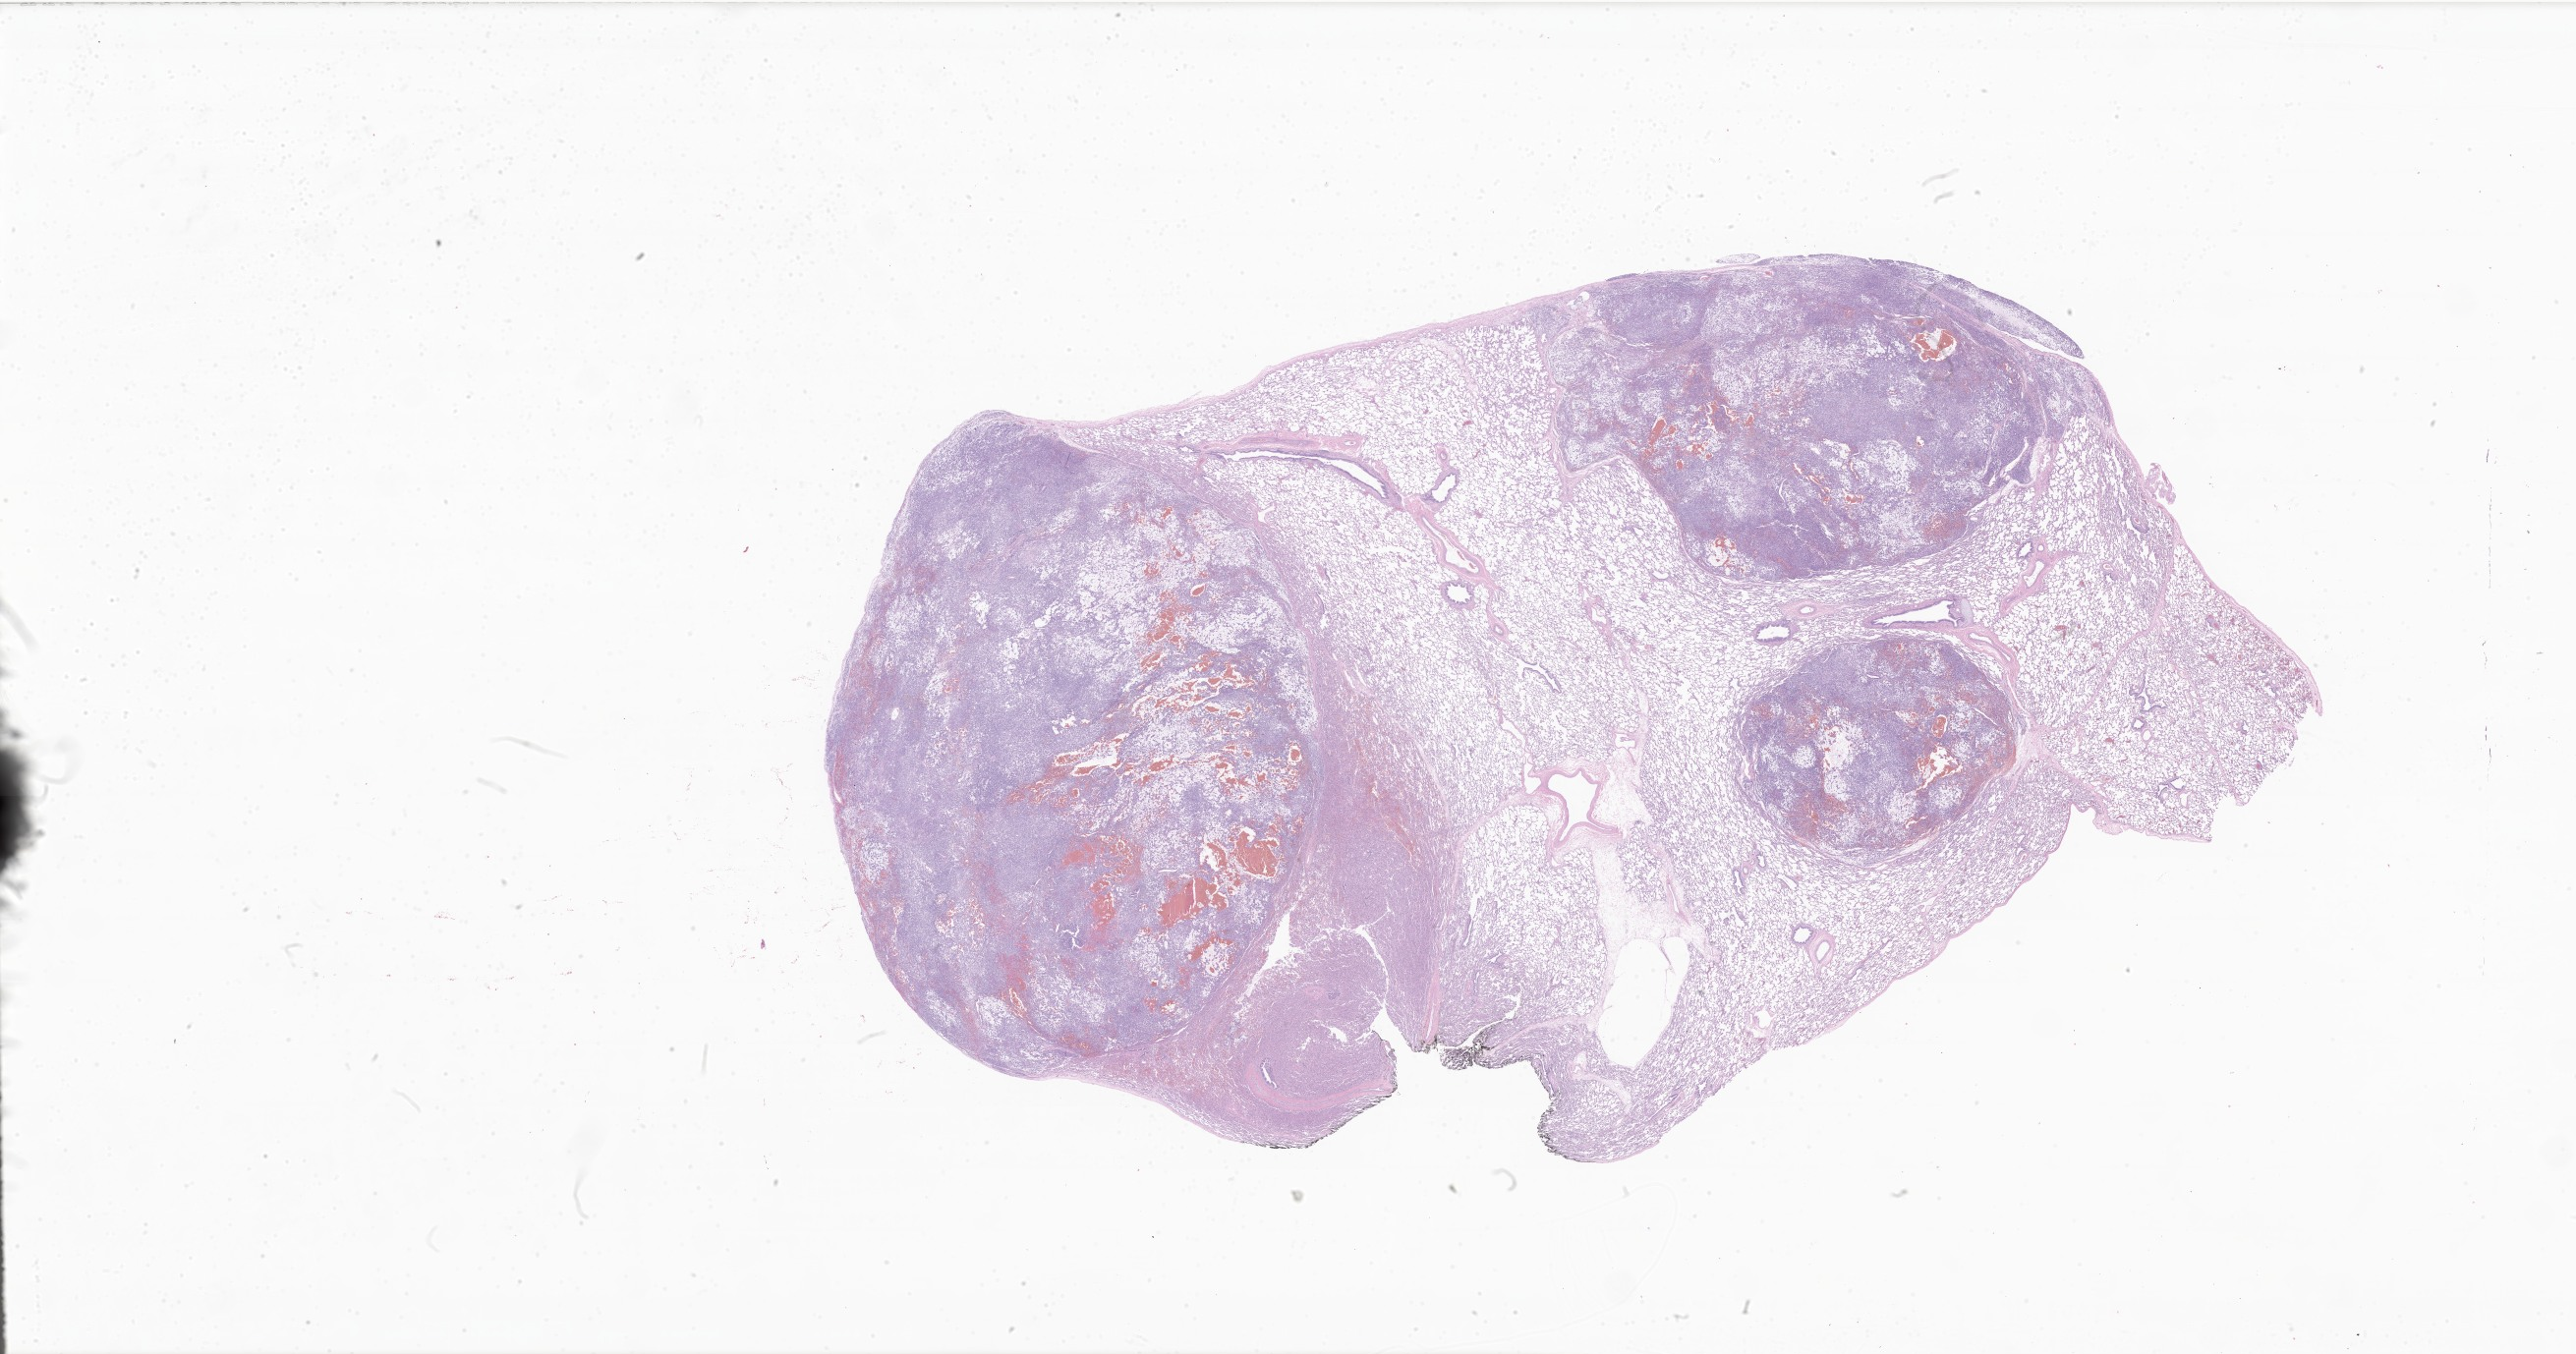
Haematoxylin and eosin whole-slide image of tumor tissue from the liver — whole scanned area (about 44.2 x 23.2 mm) shown as a low-resolution overview; formalin-fixed, paraffin-embedded (FFPE) tissue. Female patient, age 294 days.
Diagnosis (ICD-O-3 morphology term): Rhabdoid tumor, NOS.